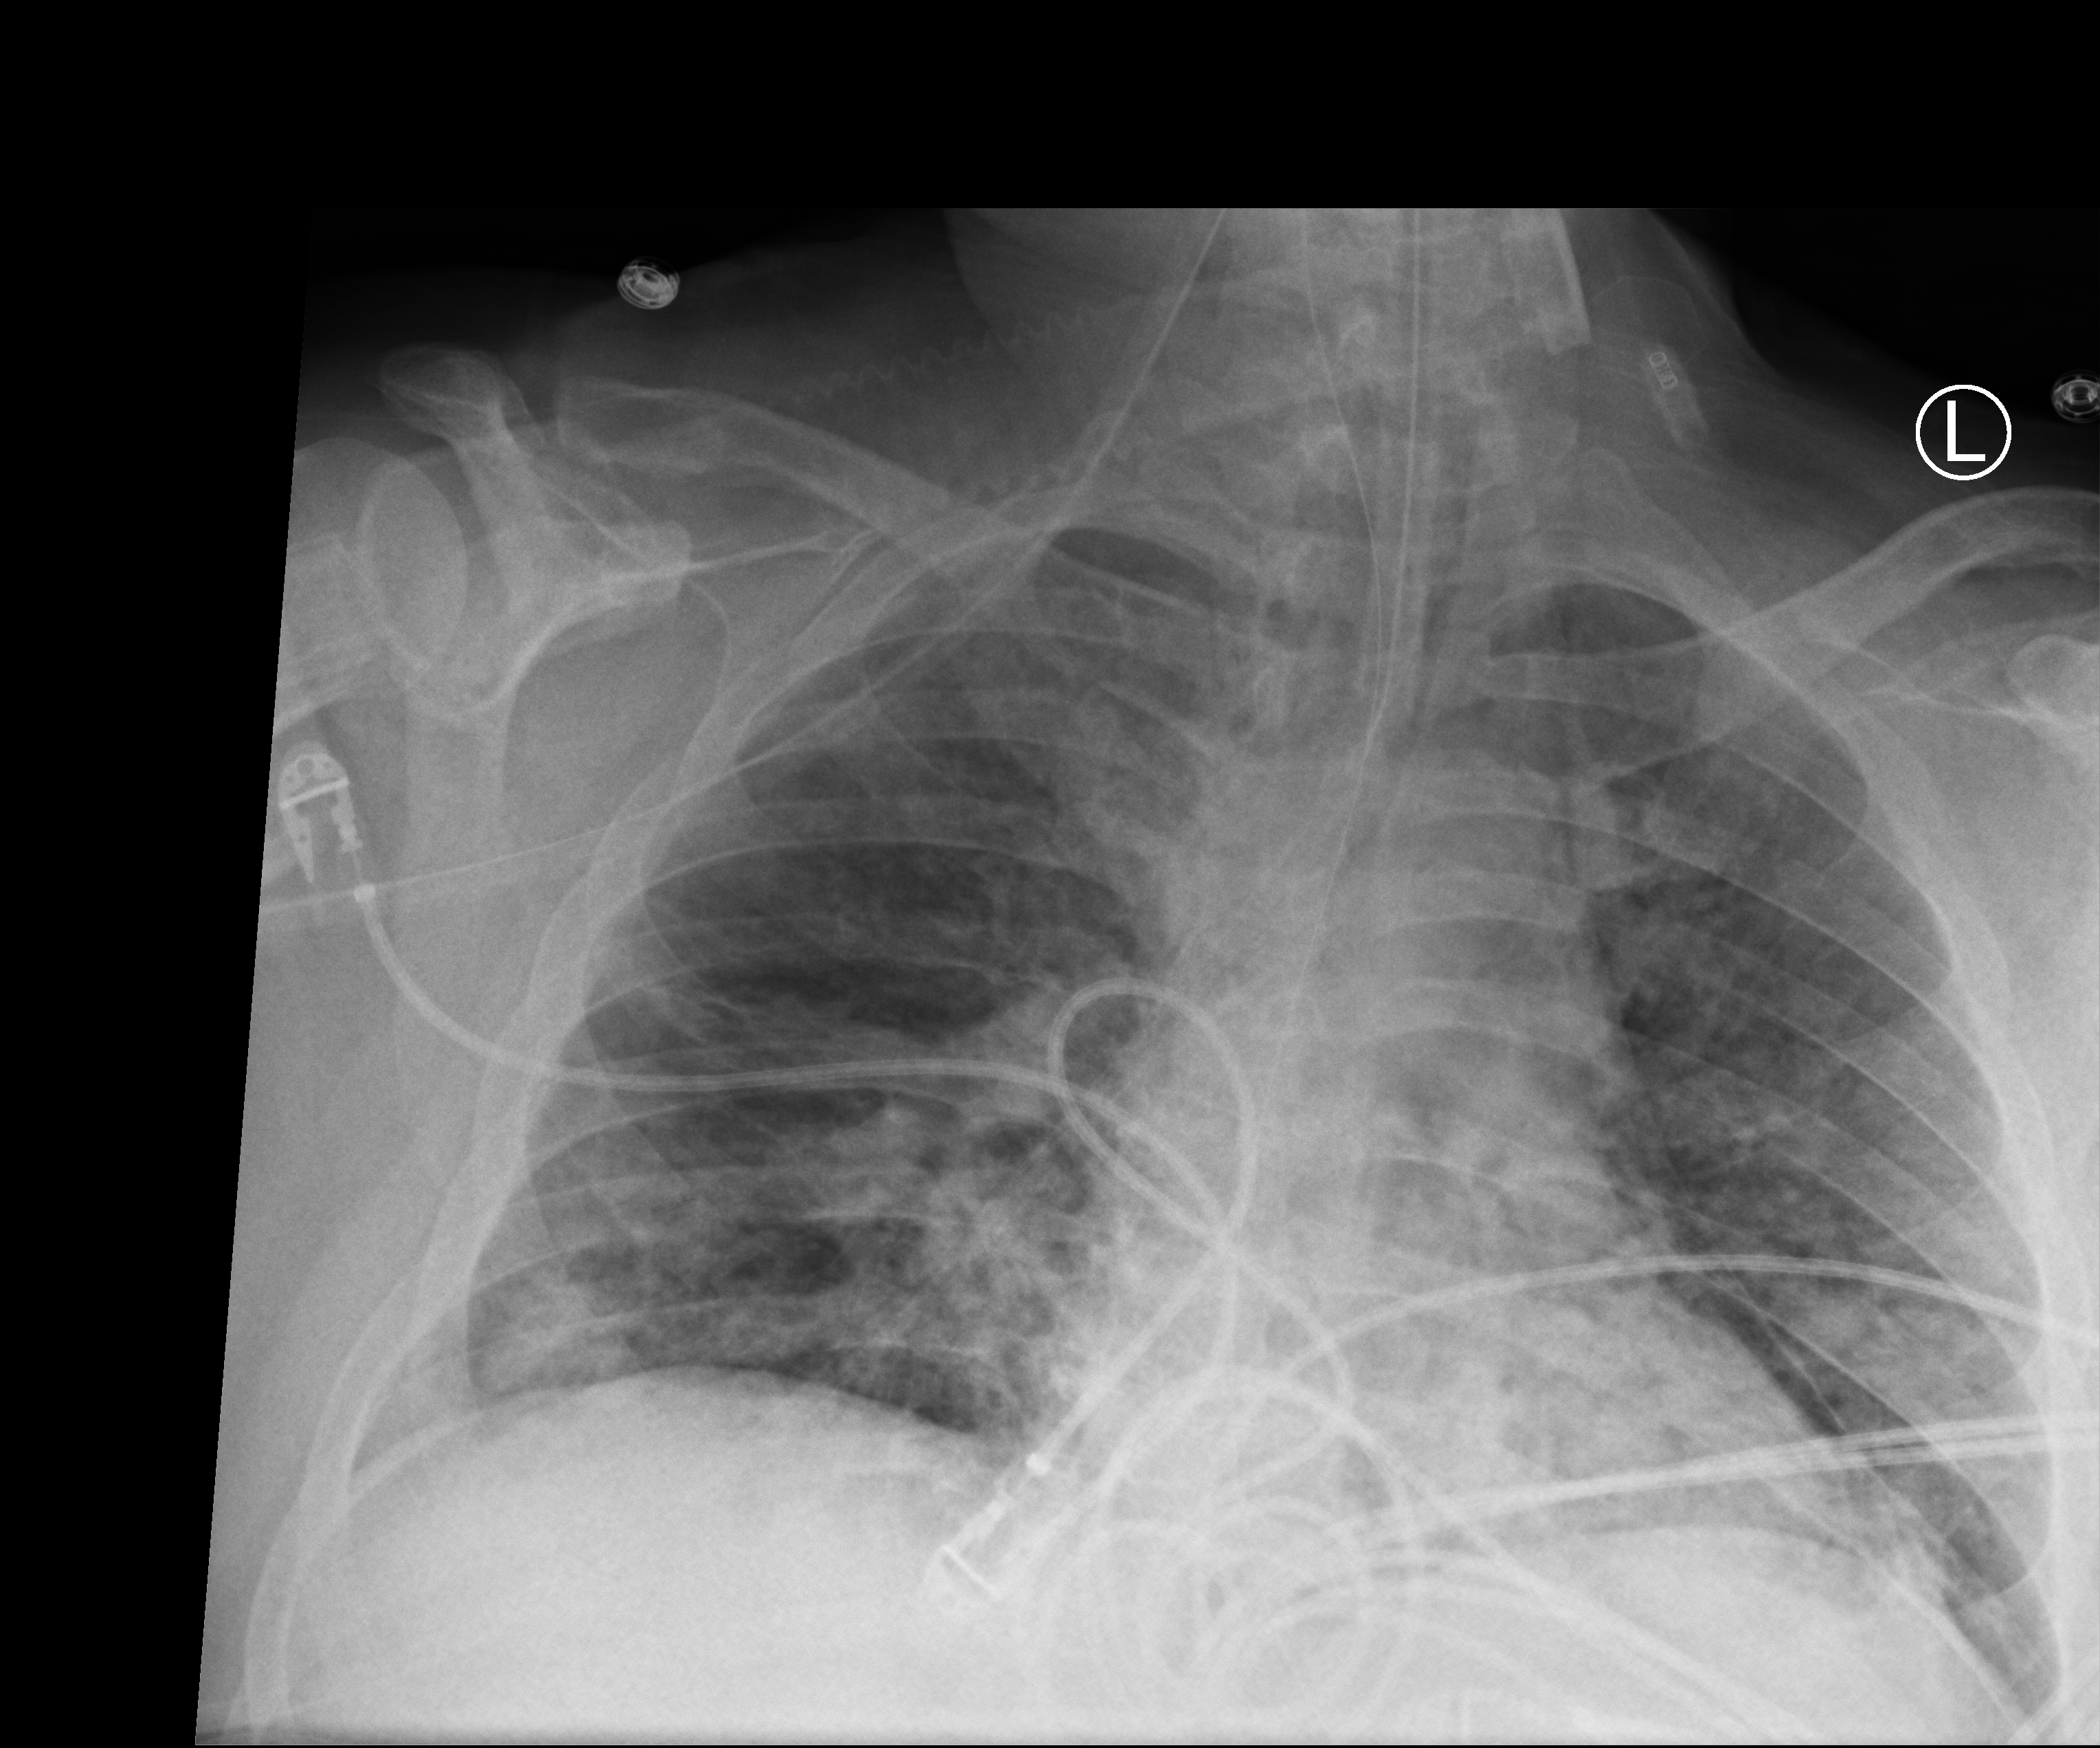
Bedside chest radiograph (computed radiography), anteroposterior (AP) projection. Patient hospitalised with COVID-19, aged 18–59 years.
Admission-level facts for this patient (not findings on this image; timing relative to this image not recorded):
- admitted to intensive care during this hospital stay: yes
- mechanically ventilated during this hospital stay: yes